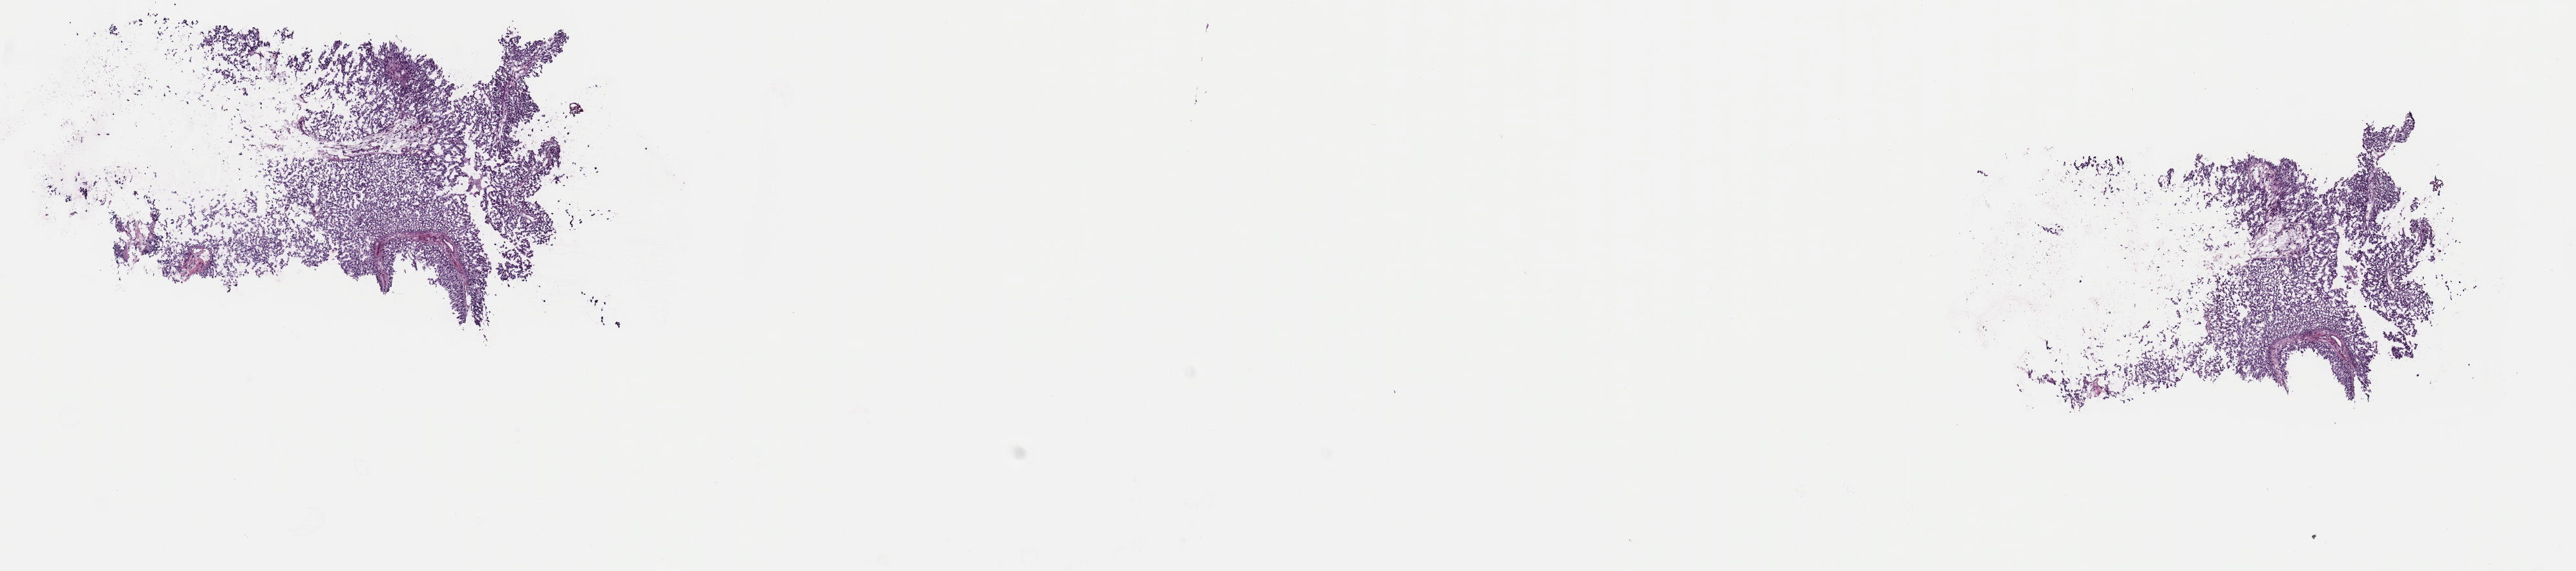
Whole-slide histology image, H&E, low-resolution overview of the scanned area, about 15.7 x 3.5 mm (from a 40x scan), frozen section, primary tumour sample from the bladder. Patient: male, age at initial diagnosis 52 years. Histologic grade: high grade. Pathologist review of this section (percent, as recorded): tumour cells 95%, tumour nuclei 99%, normal cells 0%, stromal cells 5%, necrosis 0%. Infiltration values recorded for this section: lymphocyte infiltration 0%, monocyte infiltration 0%, neutrophil infiltration 0%.
AJCC pathologic stage: II (7th edition). TNM: T2 N0 M0. Diagnosis: Papillary transitional cell carcinoma.